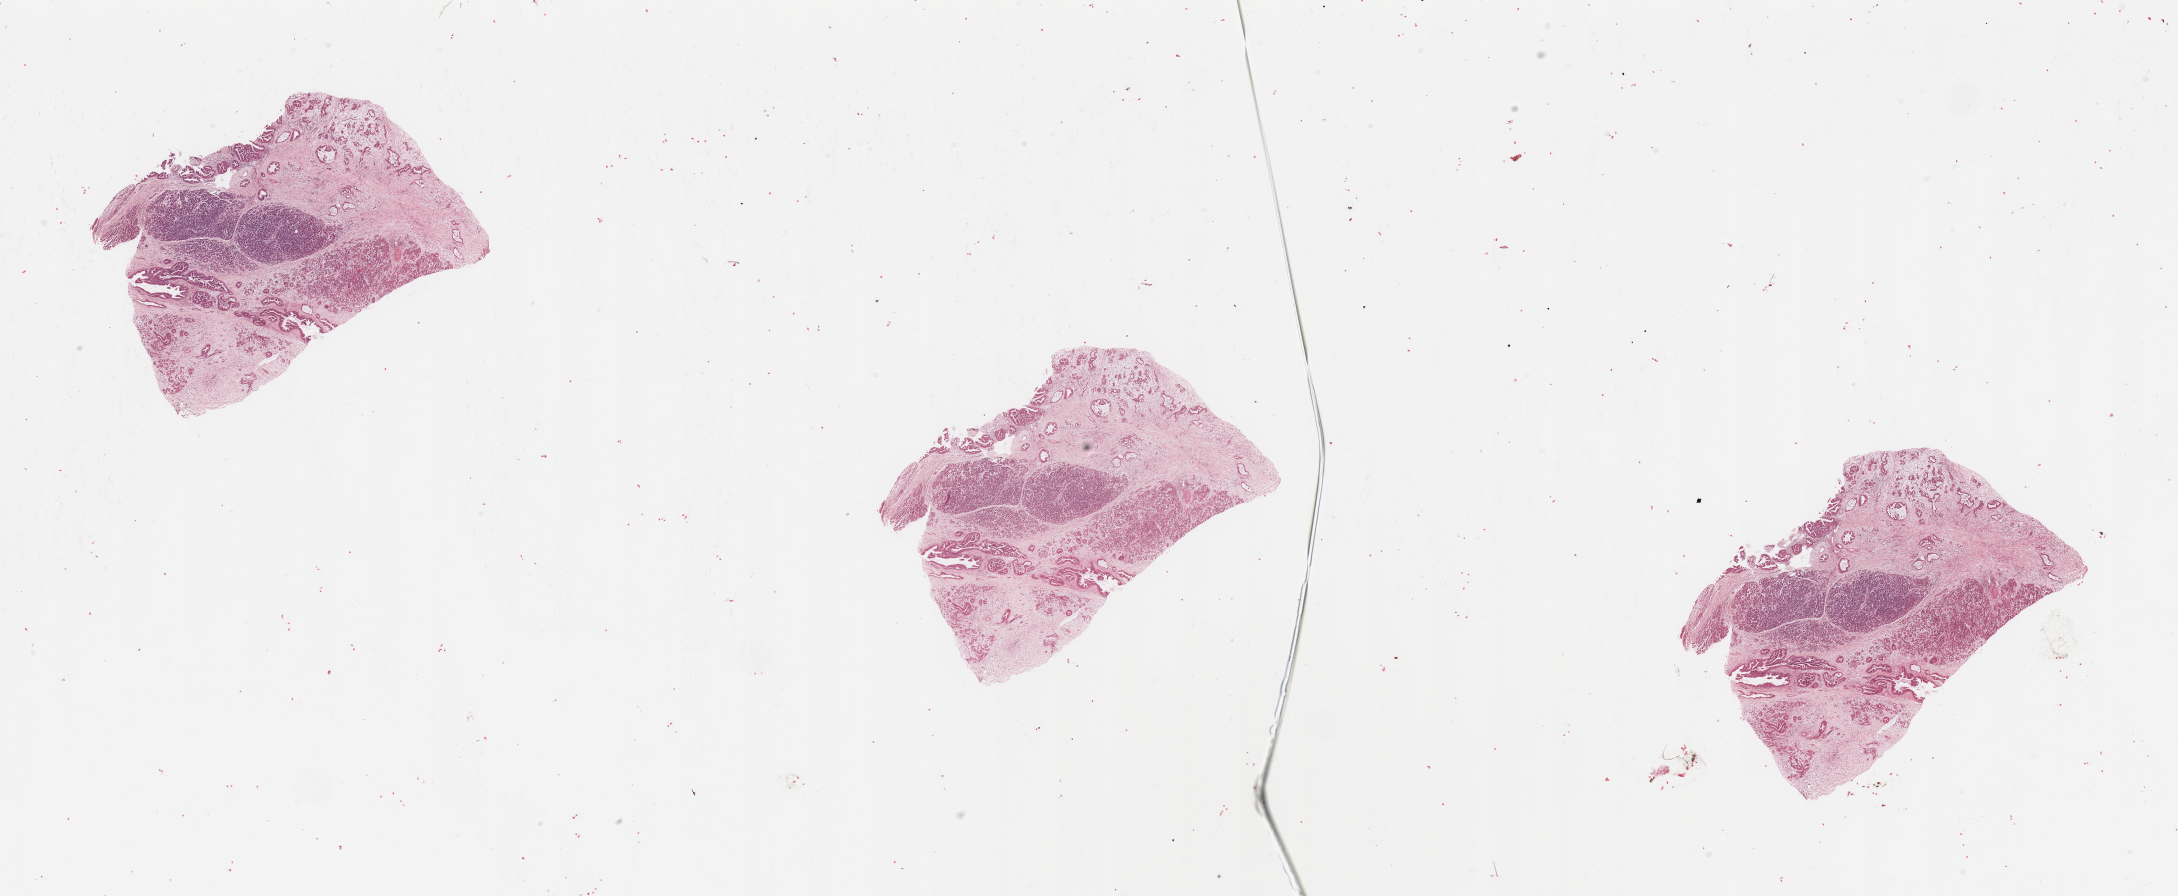
Digitized Hematoxylin and eosin (H&E) stained tissue section (whole slide), shown as a low-resolution overview of the whole scanned area (about 34.5 x 14.2 mm); tumour tissue sample, sampled site: pancreas. Female, 64 y/o. Histologic grade: G2 (moderately differentiated). Pathologist review of this section (percent, as recorded): tumour nuclei 15%, necrosis 0%.
Primary tumour site (as recorded): head. Histologic diagnosis: Infiltrating duct carcinoma, NOS. AJCC pathologic stage: IIB.